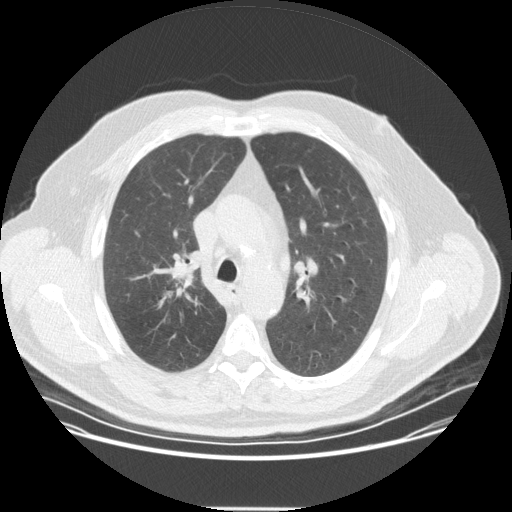
Chest CT (low-dose screening protocol), one axial image. Second screening round (one year after baseline). Lung window (W 1500 / L -600 HU). Slice 115 of 351 in the series. Male participant, aged 57 years at enrolment. Current smoker at enrolment.
Expert reader's lesion annotation, box from (x=145, y=249) to (x=211, y=313) px. Reader record for this screening exam (exam-level; its link to the box is not recorded): non-calcified nodule or mass ≥4 mm, right upper lobe, 20 × 16 mm, spiculated (stellate) margins, soft tissue attenuation, pre-existing on the prior screen: no. Official screen result: positive, other. Participant outcome: lung cancer diagnosed 35 days after this screen — non-small cell carcinoma, right upper lobe, poorly differentiated (G3), stage IIA (AJCC 6th edition), 25 mm at pathology.